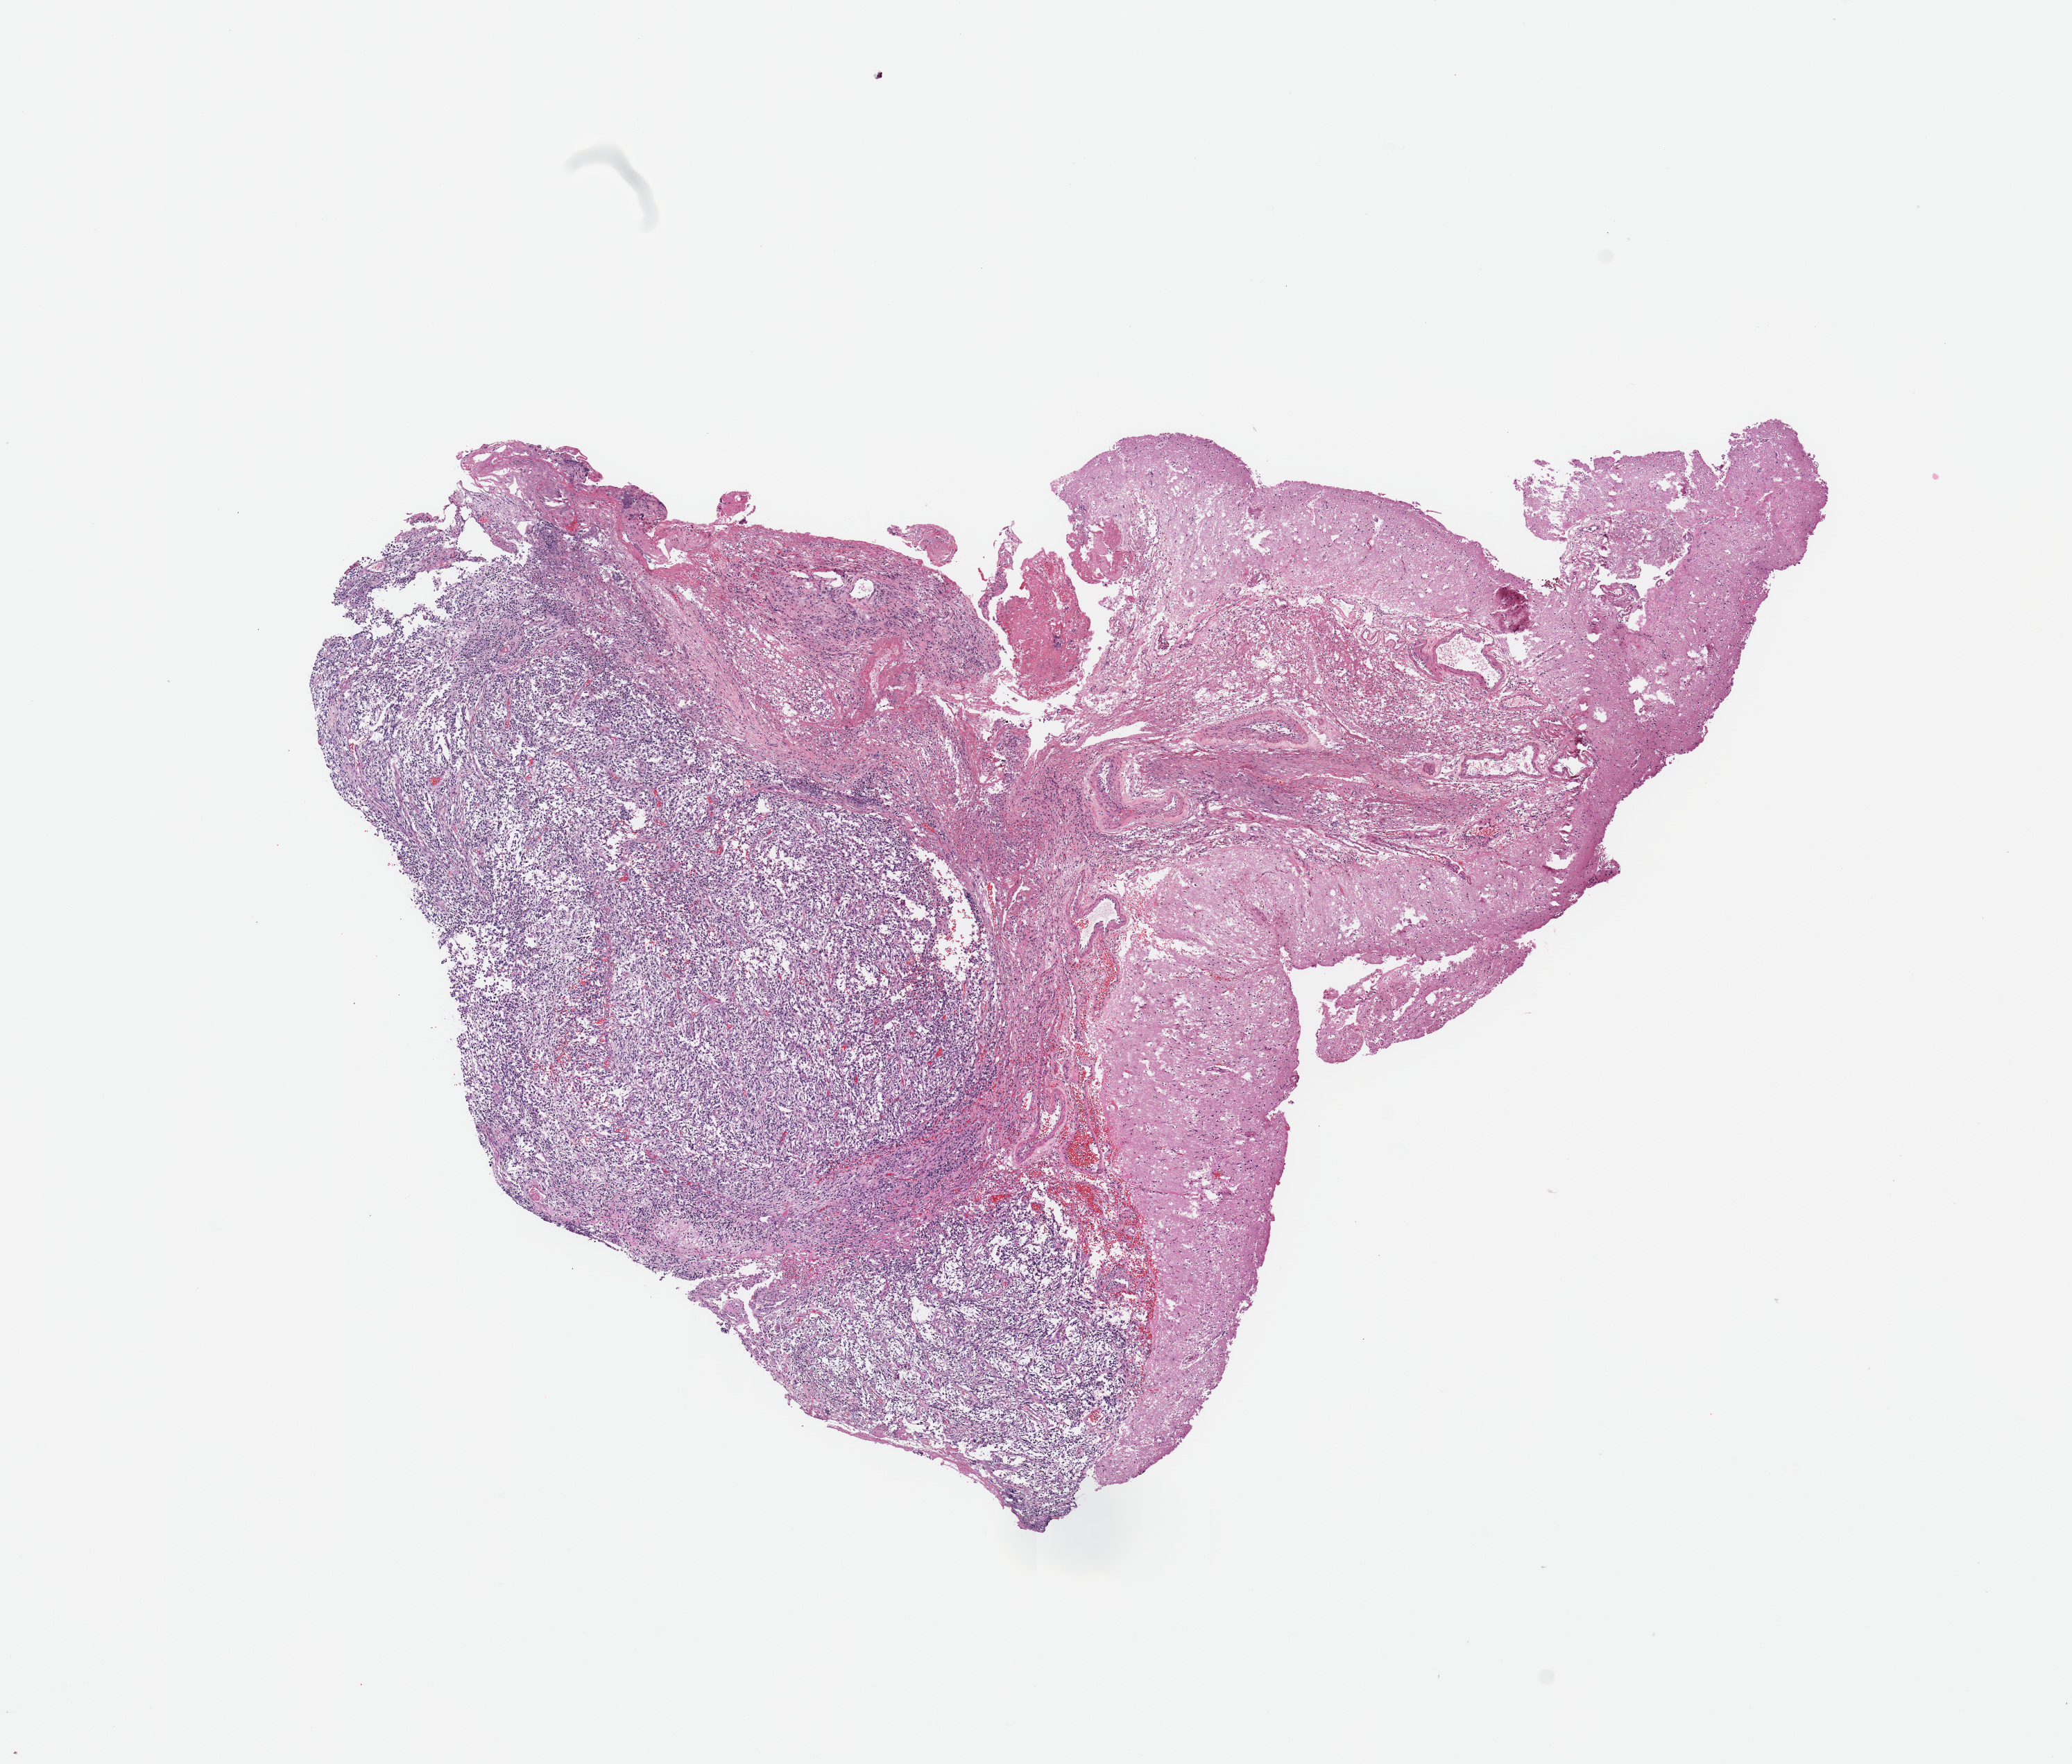
Whole-slide histology image, H&E-stained, shown as a low-resolution overview of the whole scanned area (about 11.8 x 10.1 mm, from a 20x scan). Tumour tissue sample, brain. Patient: female, age 73 years.
• histologic diagnosis: Glioblastoma